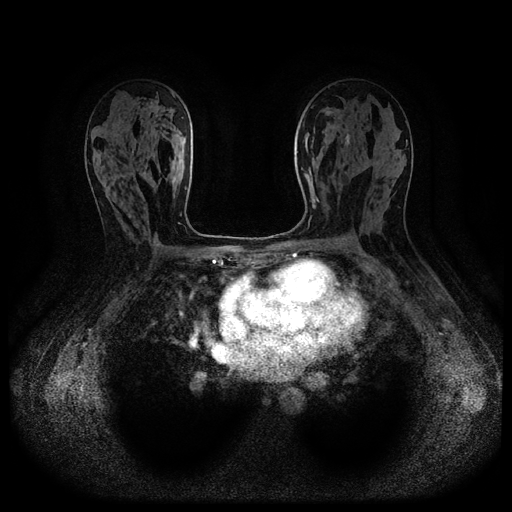
Breast MRI (dynamic contrast-enhanced, multi-phase), one axial slice. Slice 63 of 116 in the series (ordered by position). Dynamic contrast-enhanced series, time point 2 of 5 at this slice position (early post-contrast). 1.5 T. TE 2.6 ms, TR 5.3 ms. 2.2 mm slice thickness. 512 × 512 image matrix, field of view 340 × 340 mm. Patient: female, 54 years.
Outlined on this slice (semi-automatic segmentation, software-assisted and operator-edited):
- breast lesion (labelled benign in the annotation): bounding box (x1, y1, x2, y2) in pixels: (345, 126, 350, 145)